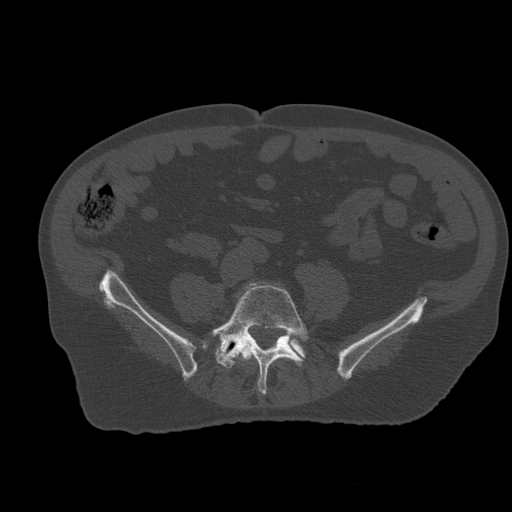
CT including the spine, one axial slice. Position 143 of 399 along the scan axis. Reconstruction kernel STANDARD. 120 kVp. Bone window (W 1800 / L 400 HU). 512 × 512 image matrix. Patient age 73 years. Case-level facts recorded for this patient, not image findings: primary cancer: prostate.
Outlined on this slice (semi-automatically segmented with operator editing):
- L4 vertebra: bounding box [x1, y1, x2, y2] px = [237, 345, 258, 362]
- L5 vertebra: [211, 283, 309, 395]